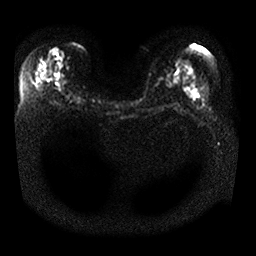
Breast MRI, one axial slice. Position 18 of 25 along the scan axis. Diffusion-weighted series; image 2 of 4 stored at this slice position (different b-values; order by instance number). 1.5 T. 4 mm slice thickness. 256 × 256 image matrix. Female patient.
Structures marked on this image (expert manual segmentation):
- tumour on diffusion-weighted imaging: box from (x=50, y=47) to (x=65, y=62) px